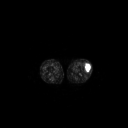
FDG PET of an extremity soft-tissue mass (from a PET/CT study), one axial slice. Position 173 of 223 along the scan axis. 3.27 mm slice thickness. 128 × 128 image matrix, field of view 700 × 700 mm. Patient: female, 16 years. From the clinical record (not read from this slice): histological type: spindle cell suggestive of biphasic synovial sarcoma; grade: intermediate; site of the primary tumour: left knee.
Outlined on this slice (expert contour drawn on MRI and transferred to this co-registered scan by the dataset authors):
- gross tumour volume including surrounding oedema: bounding box <84,62,90,72> (left, top, right, bottom; pixels)
- gross tumour volume (mass): <85,62,90,72>